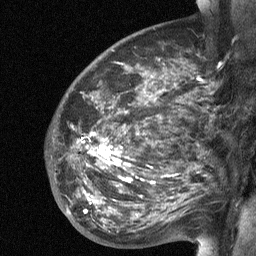
Breast MRI (dynamic contrast-enhanced), one sagittal slice. Slice 41 of 64 in the series (ordered by position). Dynamic contrast-enhanced study with each time point stored as its own series, time point 2 of 3 at this slice position (early post-contrast, ordered by acquisition time). 1.5 T. TE 4.8 ms, TR 27 ms. 2 mm slice thickness. 256 × 256 image matrix, field of view 200 × 200 mm. Patient: female, 50 years. From the clinical record (not read from this slice): setting: breast cancer imaged before/during neoadjuvant chemotherapy; receptor status: HER2-positive.
Annotated regions visible in this slice (semi-automatic segmentation, software-assisted and operator-edited):
- analysis volume of interest (the breast-tissue region the enhancement analysis was run in; not a lesion): bounding box (x1, y1, x2, y2) in pixels: (53, 91, 203, 227)
- tumour enhancement mask (voxels above the 90 % enhancement threshold inside the analysis volume of interest): (98, 147, 130, 181)